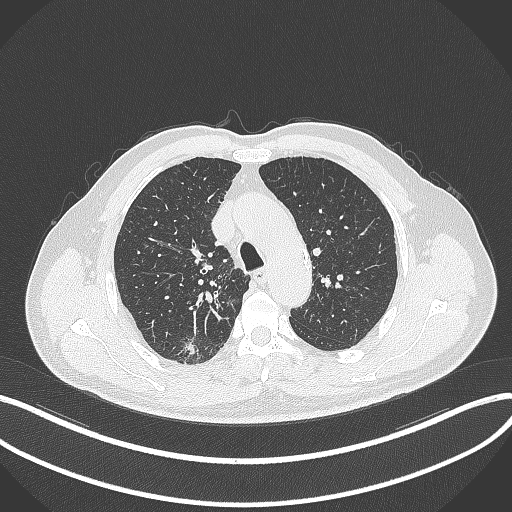
Chest CT, one axial slice; position 275 of 359 along the scan axis; reconstruction kernel B70f; 120 kVp; lung window (W 1500 / L -600 HU); 1 mm slice thickness; 512 × 512 image matrix. Male patient, age 69 years. From the clinical record (not read from this slice): clinical TNM (as recorded): T1b N0 M0; histopathological grade: G2-3.
Structures marked on this image (rectangle marked by the reading radiologist):
- lung tumour (recorded histology: adenocarcinoma): bounding box (x1, y1, x2, y2) in pixels: (178, 337, 202, 361)